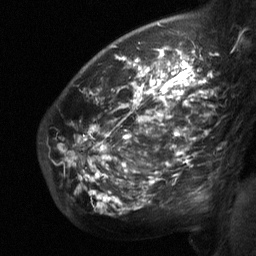
Breast MRI (dynamic contrast-enhanced), one sagittal slice; position 46 of 64 along the scan axis; dynamic contrast-enhanced study with each time point stored as its own series, time point 2 of 3 at this slice position (early post-contrast, ordered by acquisition time); 1.5 T; TE 4.8 ms, TR 27 ms; 256 × 256 image matrix, field of view 200 × 200 mm. Female patient, age 50 years. Case-level facts recorded for this patient, not image findings: setting: breast cancer imaged before/during neoadjuvant chemotherapy; receptor status: HER2-positive.
Structures marked on this image (semi-automatically segmented with operator editing):
- analysis volume of interest (the breast-tissue region the enhancement analysis was run in; not a lesion): bounding box (x1, y1, x2, y2) in pixels: (62, 62, 213, 211)
- tumour enhancement mask (voxels above the 90 % enhancement threshold inside the analysis volume of interest): (72, 62, 213, 202)